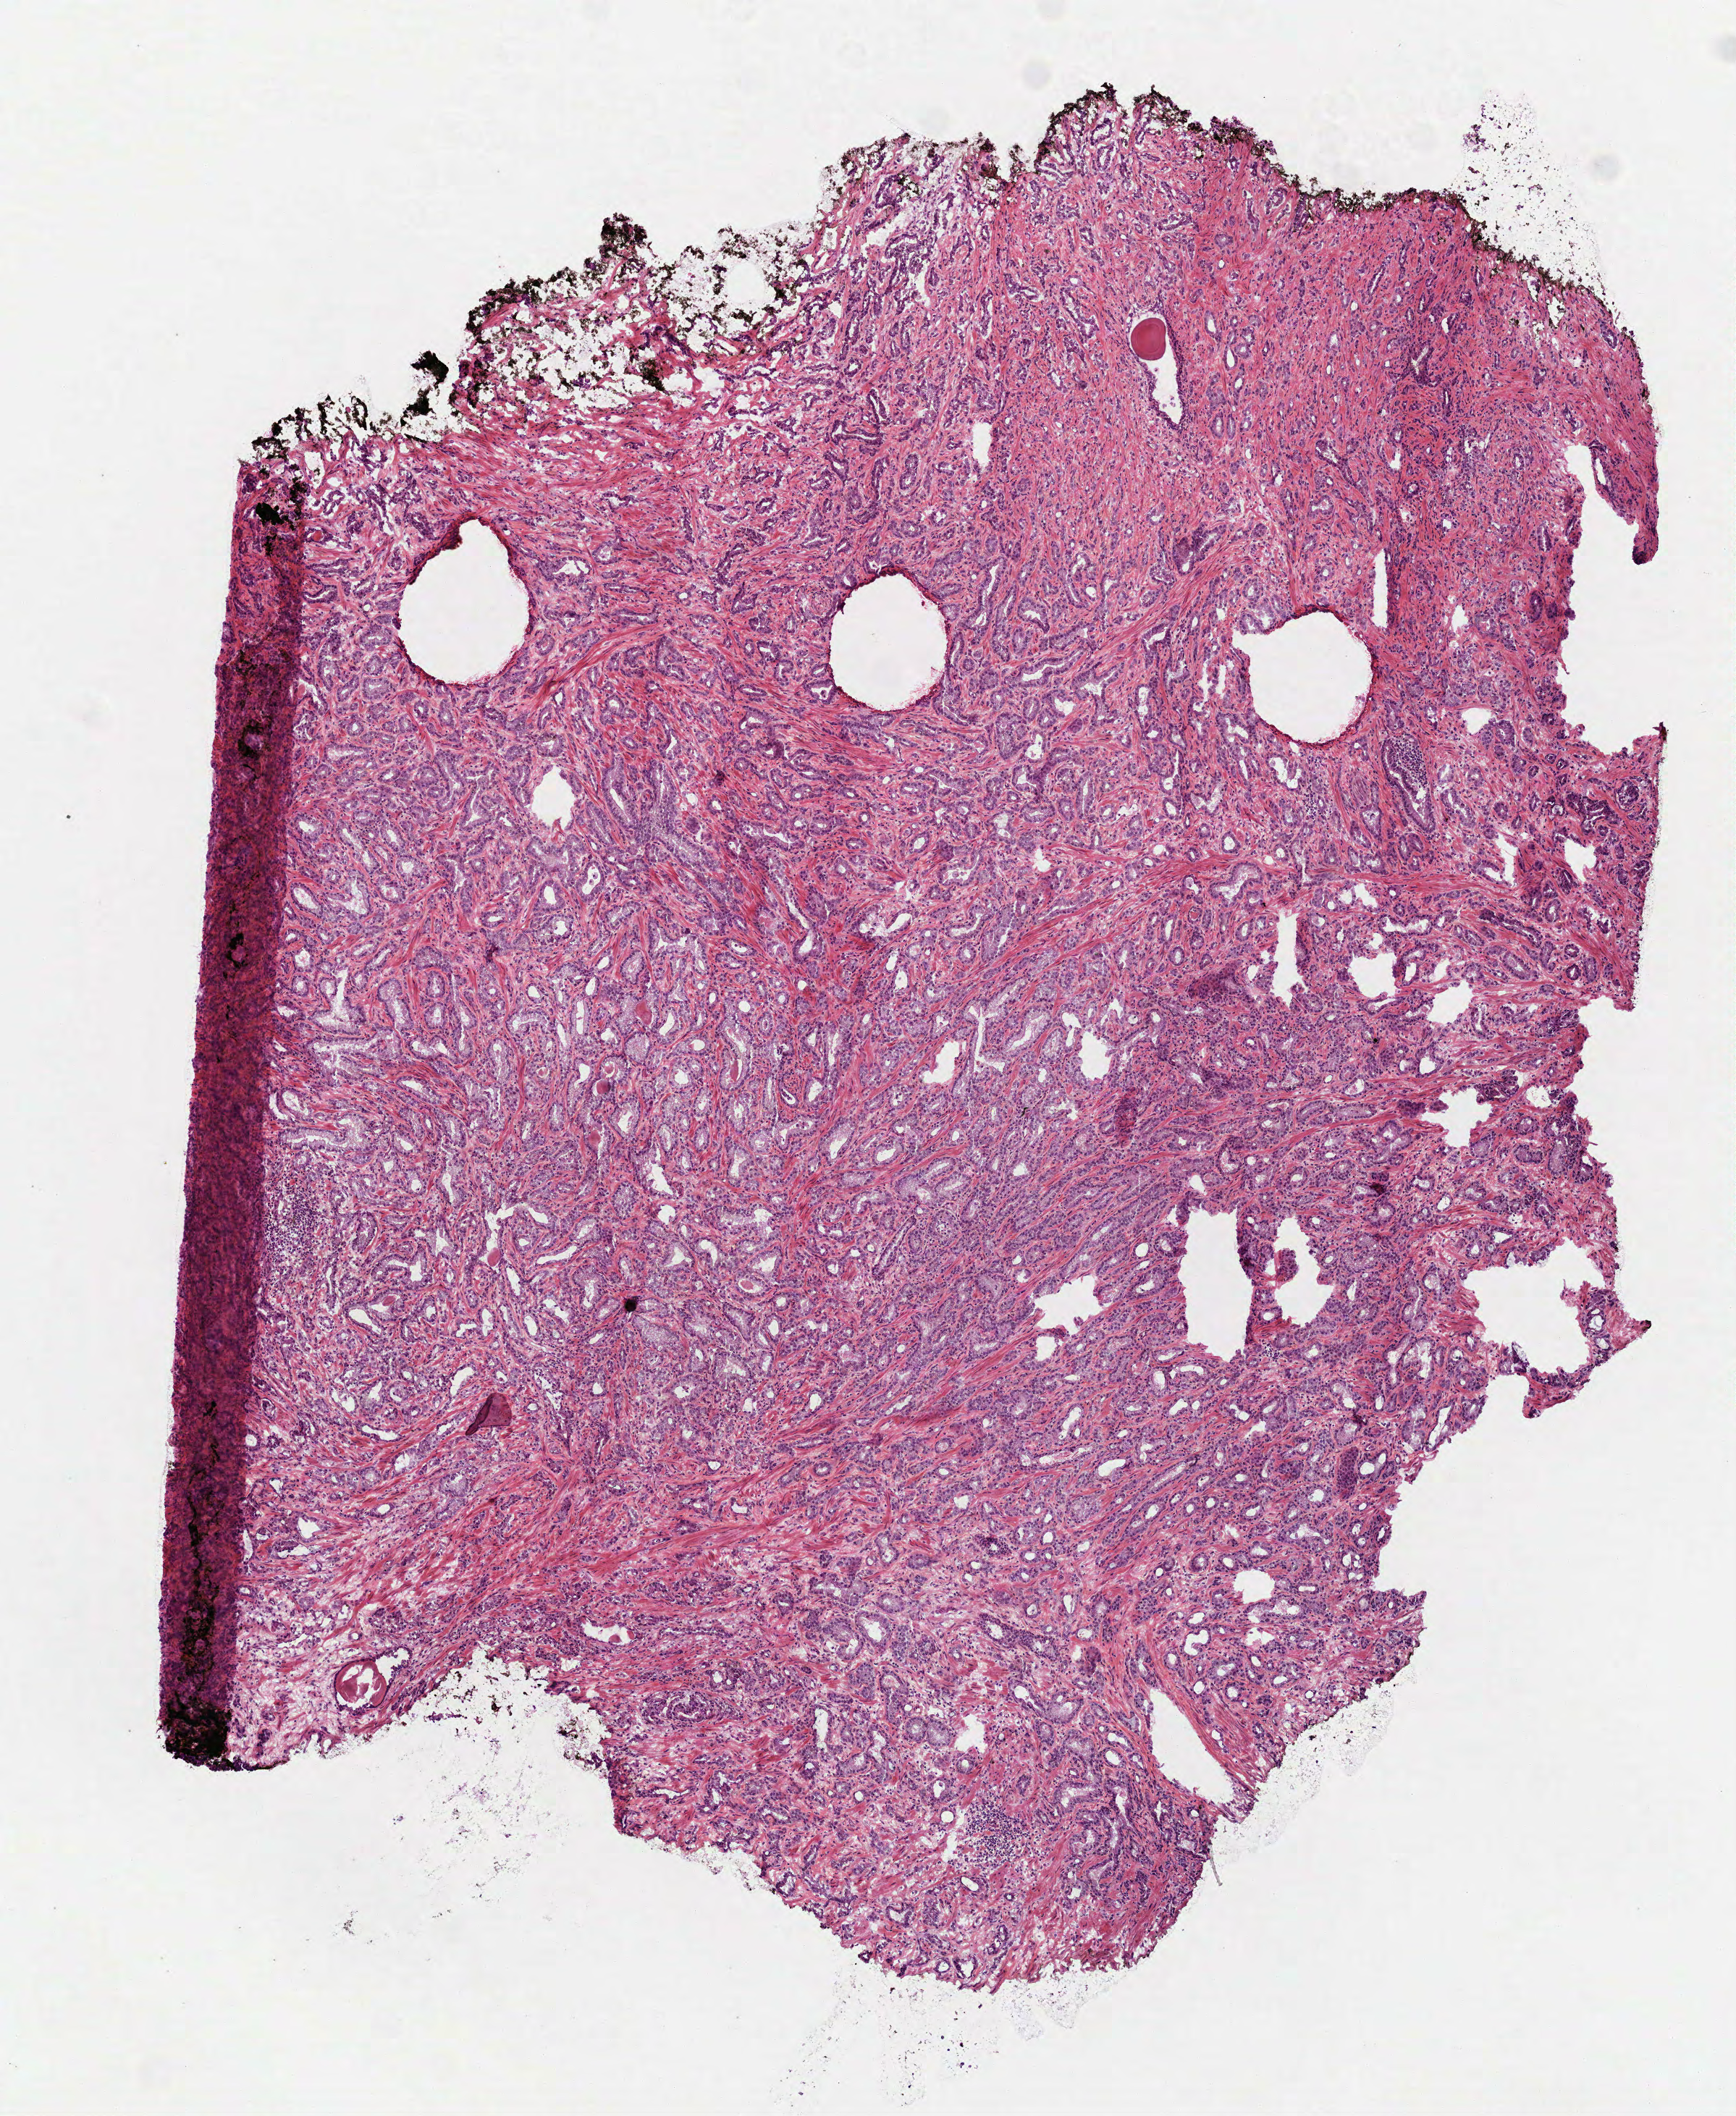
Hematoxylin and eosin (H&E) stained whole-slide image — a low-resolution overview of the entire scanned area, about 4.8 x 5.9 mm. Frozen section from the top of the tissue portion. Prostate, primary tumour sample. Male, age 73 years at initial diagnosis. Gleason score: 7 (4+3). Pathologist review of this section (percent, as recorded): tumour nuclei 80%, necrosis 0%.
- diagnosis: Acinar cell carcinoma (prostate gland)
- lymph nodes positive (case pathology): 0 of 2 examined